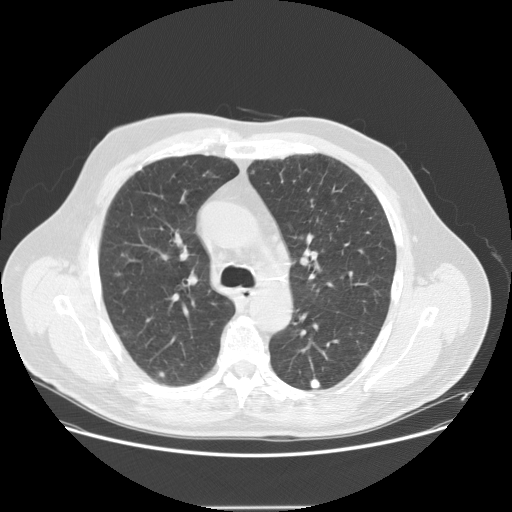
Low-dose screening chest CT, one axial slice. Slice 98 of 143 in the series (ordered by position). 120 kVp. Lung window (W 1500 / L -600 HU). 2.5 mm slice thickness. 512 × 512 image matrix, field of view 400 × 400 mm.
Structures marked on this image (outlined manually by an expert reader):
- lesion 2 (tumor): box from (x=310, y=378) to (x=321, y=389) px
- lesion 6 (tumor, lower lobe of right lung): (x=159, y=372)–(x=165, y=378)